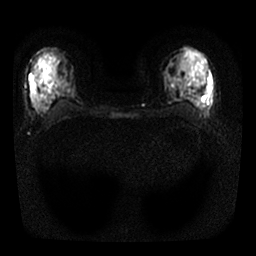
Breast MRI, one axial slice; position 12 of 25 along the scan axis; diffusion-weighted series; image 2 of 4 stored at this slice position (different b-values; order by instance number); 1.5 T; 256 × 256 image matrix, field of view 300 × 300 mm. Female patient.
Annotated regions visible in this slice (manually delineated by an expert):
- tumour on diffusion-weighted imaging: bounding box [x1, y1, x2, y2] px = [32, 75, 35, 105]